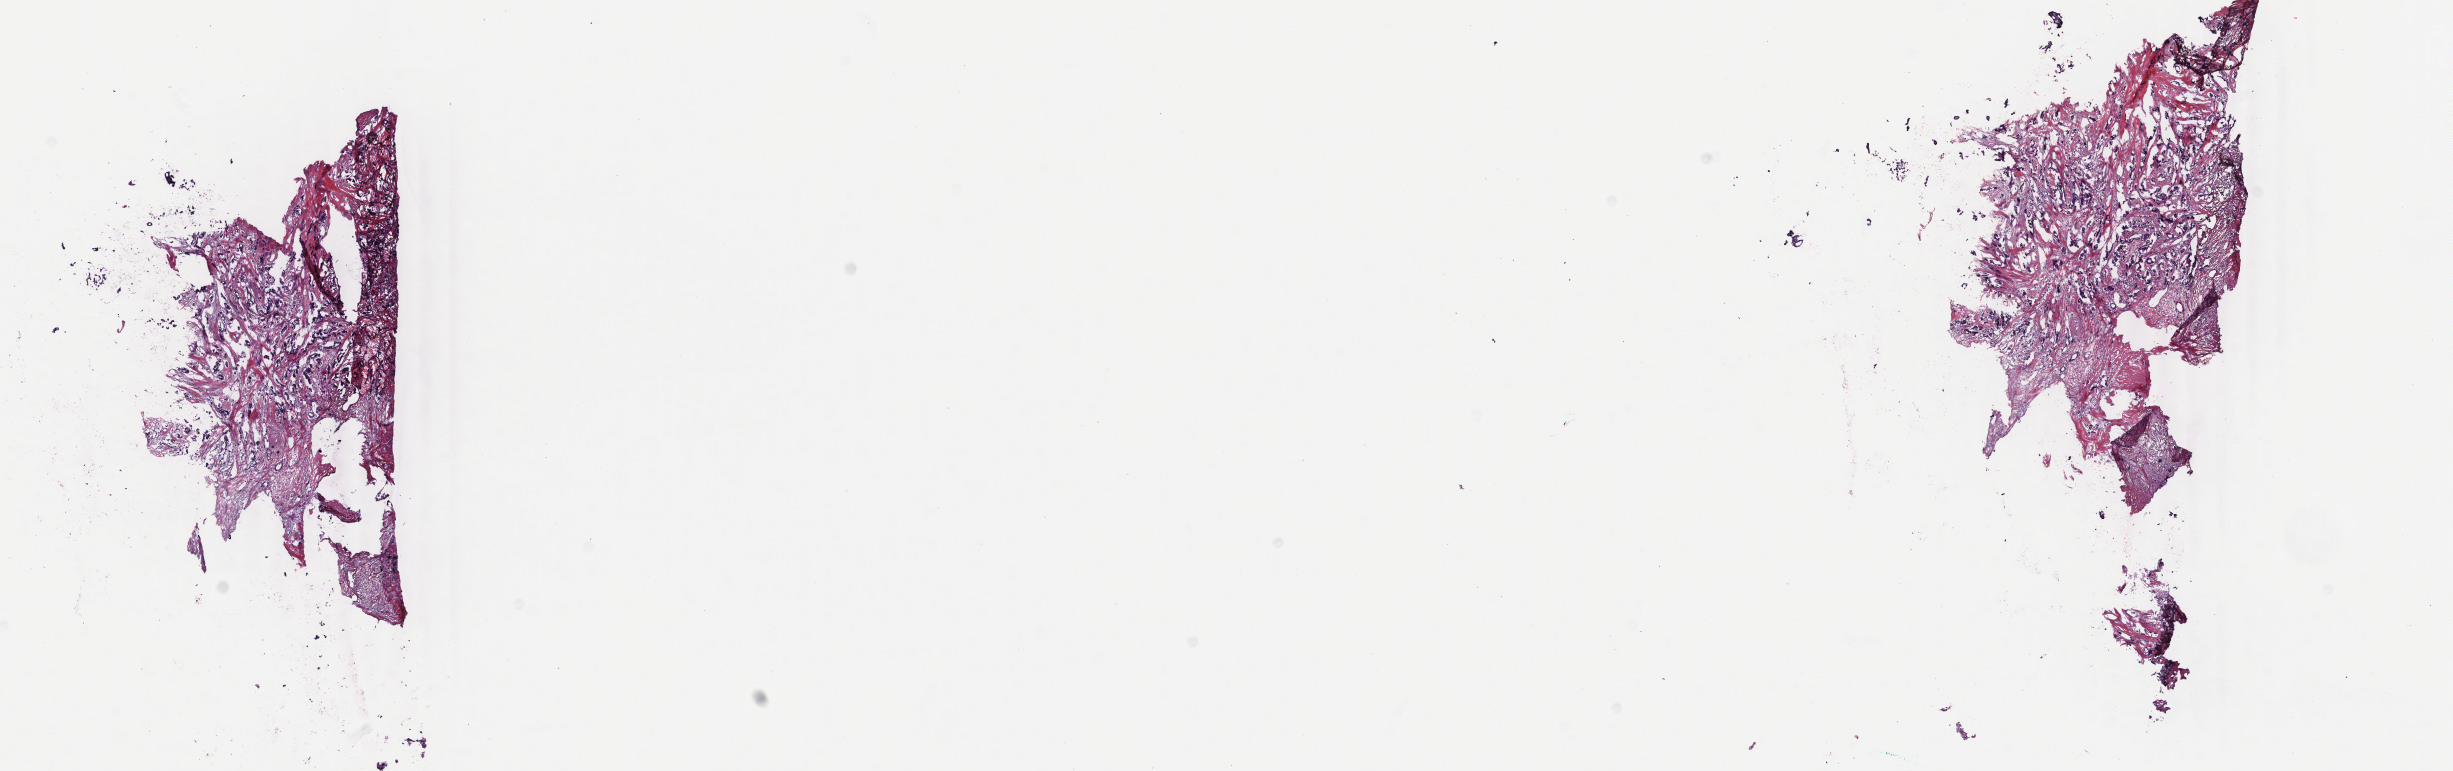
Digitized H&E-stained tissue section (whole slide), low-resolution overview of the scanned area, about 19.5 x 6.1 mm, frozen section from the bottom of the tissue portion, breast, primary tumour sample. Patient: female, age at initial diagnosis 50 years. Slide review estimates, as recorded: tumour cells 75%, tumour nuclei 75%, normal cells 0%, stromal cells 25%, necrosis 0%. Inflammatory infiltration, as recorded: lymphocyte infiltration 2%, monocyte infiltration 1%, neutrophil infiltration 1%.
AJCC pathologic stage: II (4th edition). Lymph nodes positive (case pathology): 11 of 21 examined. Pathologic diagnosis: Infiltrating duct carcinoma, NOS.